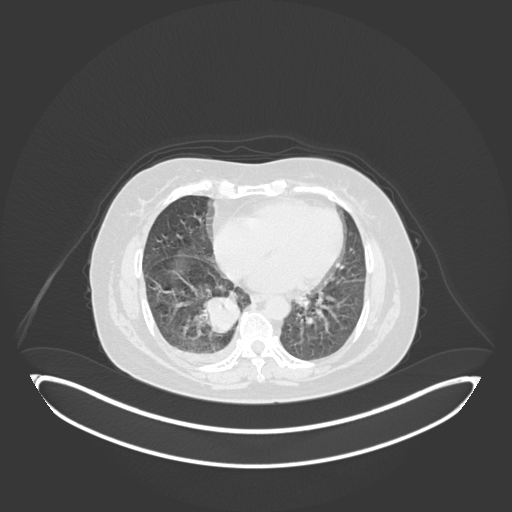
Chest CT, one axial slice. 120 kVp. Lung window (W 1500 / L -600 HU). 1 mm slice thickness. 512 × 512 image matrix, field of view 500 × 500 mm. Patient: female, 56 years. Case-level facts recorded for this patient, not image findings: clinical TNM (as recorded): T2b N1 M0.
Outlined on this slice (rectangle marked by the reading radiologist):
- lung tumour (recorded histology: small cell carcinoma): bounding box (x1, y1, x2, y2) in pixels: (205, 293, 244, 337)